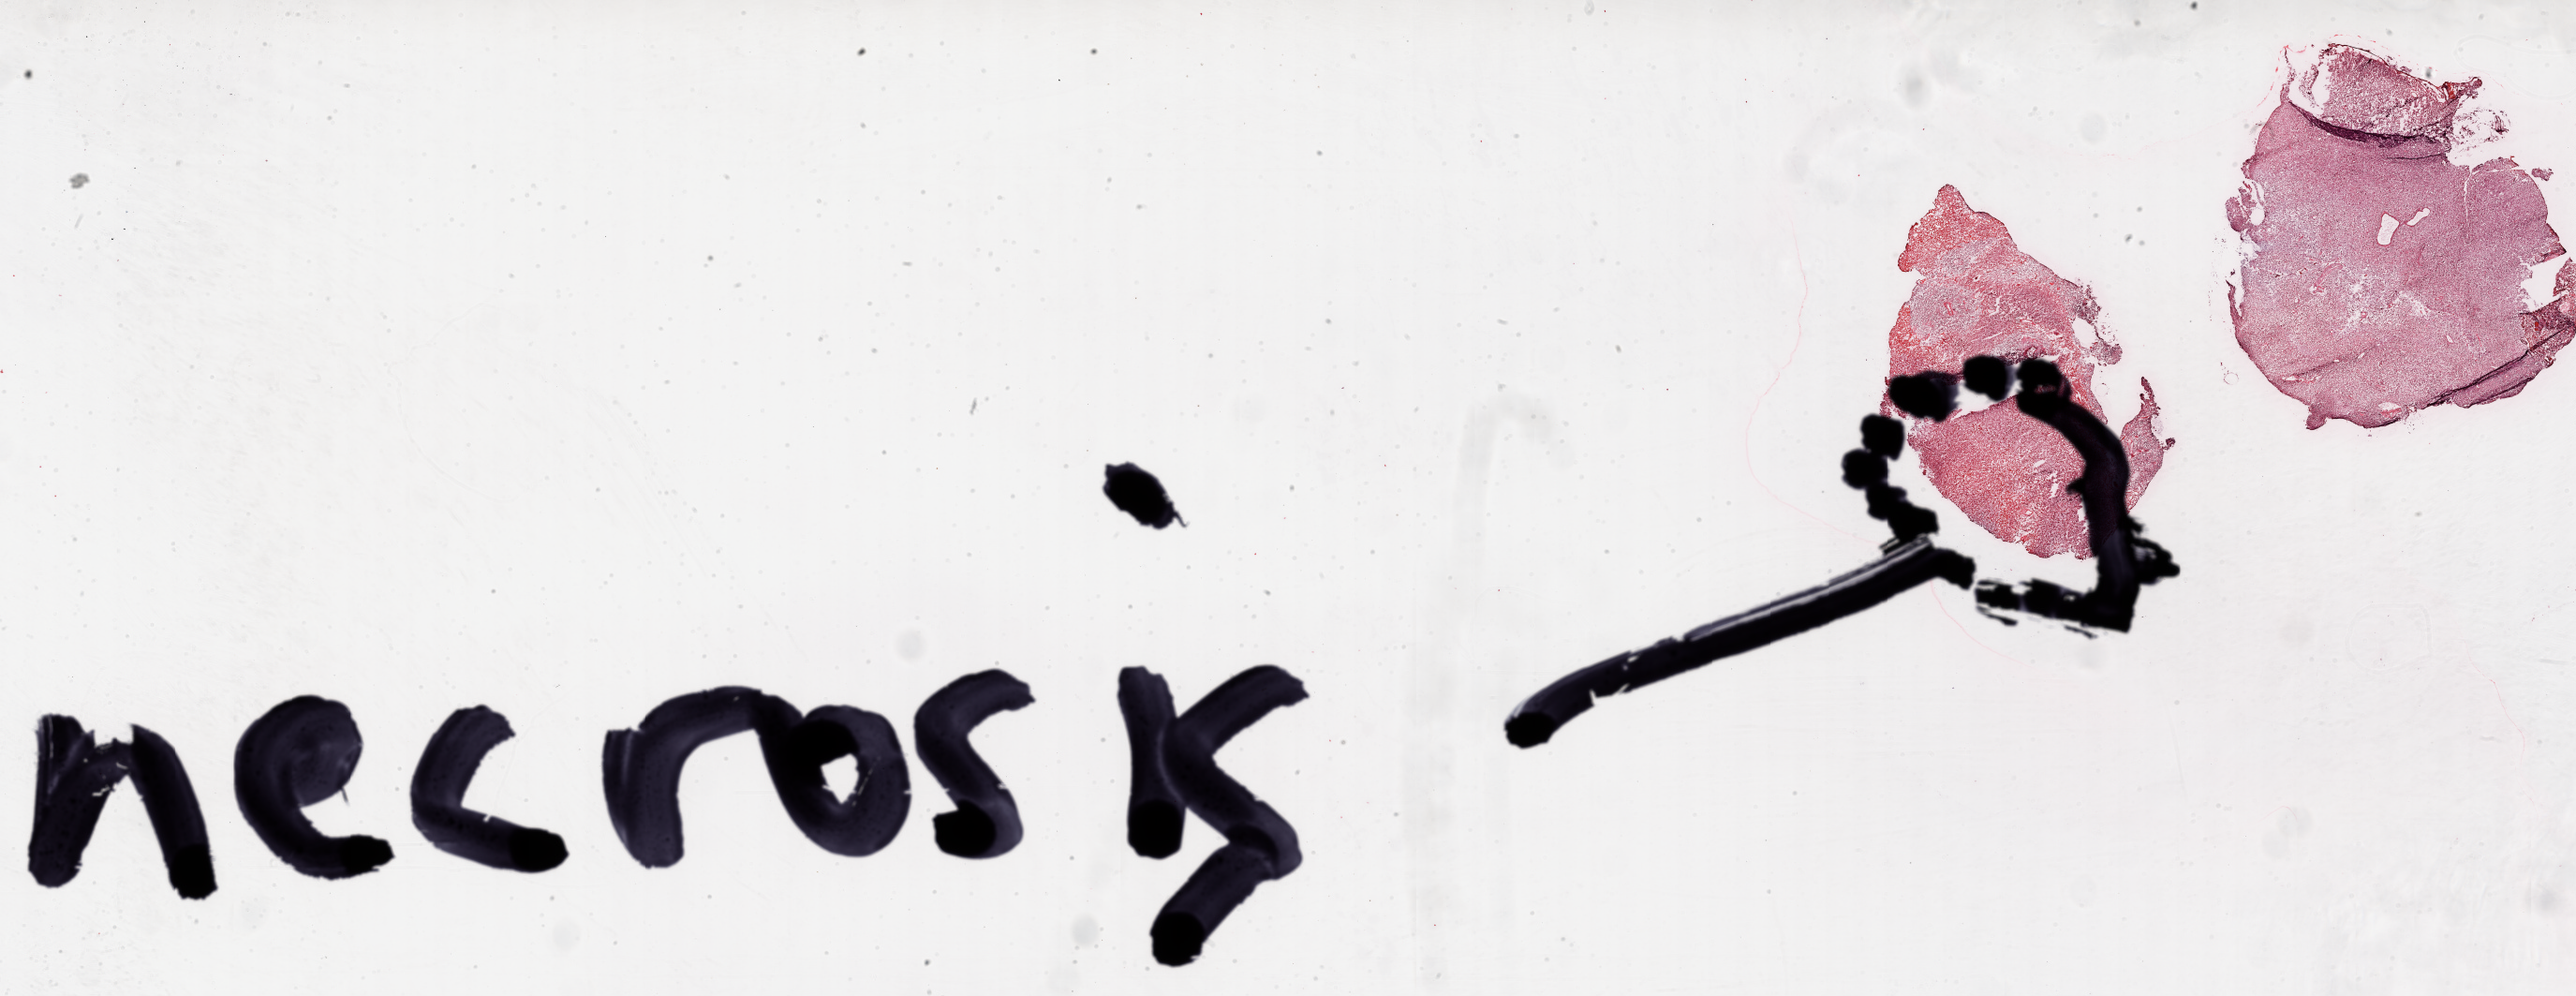
H&E whole-slide image — whole scanned area (about 44.1 x 17.1 mm) shown as a low-resolution overview. Frozen section. Sample: primary tumour, brain. Patient: male, age at initial diagnosis 78 years. Pathologist review of this section (percent, as recorded): tumour cells 65%, tumour nuclei 95%, normal cells 0%, stromal cells 0%, necrosis 35%.
Pathologic diagnosis: Glioblastoma.